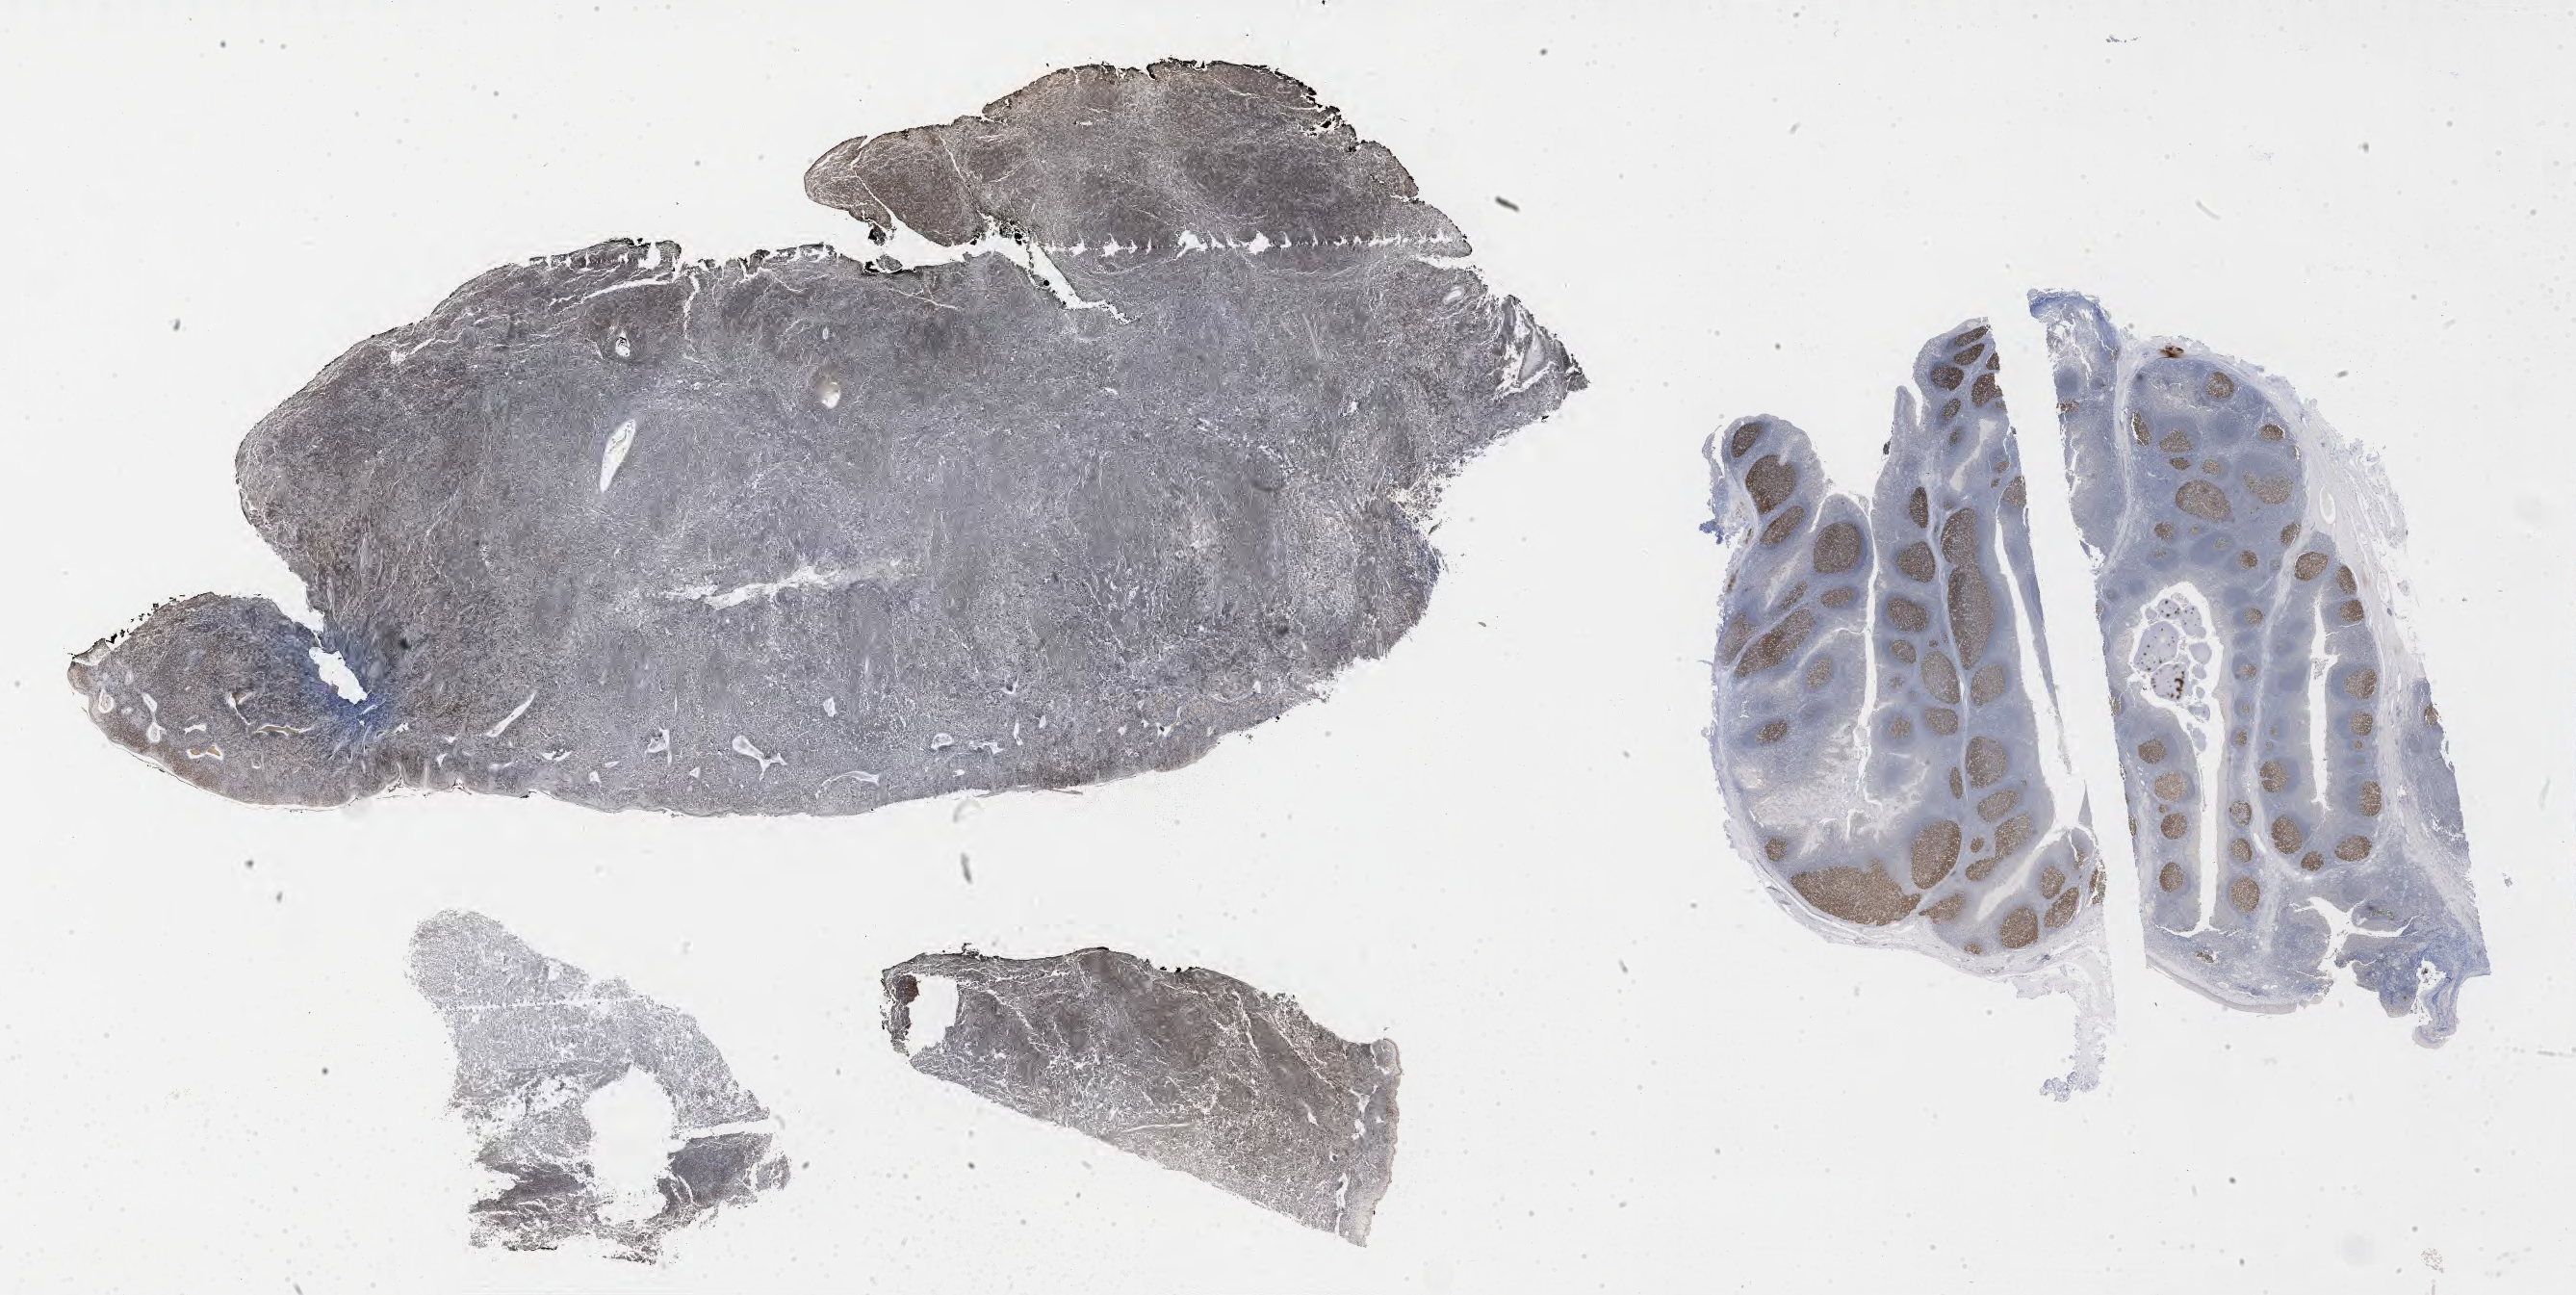
IHC for BCL6, whole-slide image — whole scanned area (about 43.3 x 21.7 mm) shown as a low-resolution overview; tumor tissue. Patient: male, 46 years old.
Diagnosis: Burkitt lymphoma, NOS.